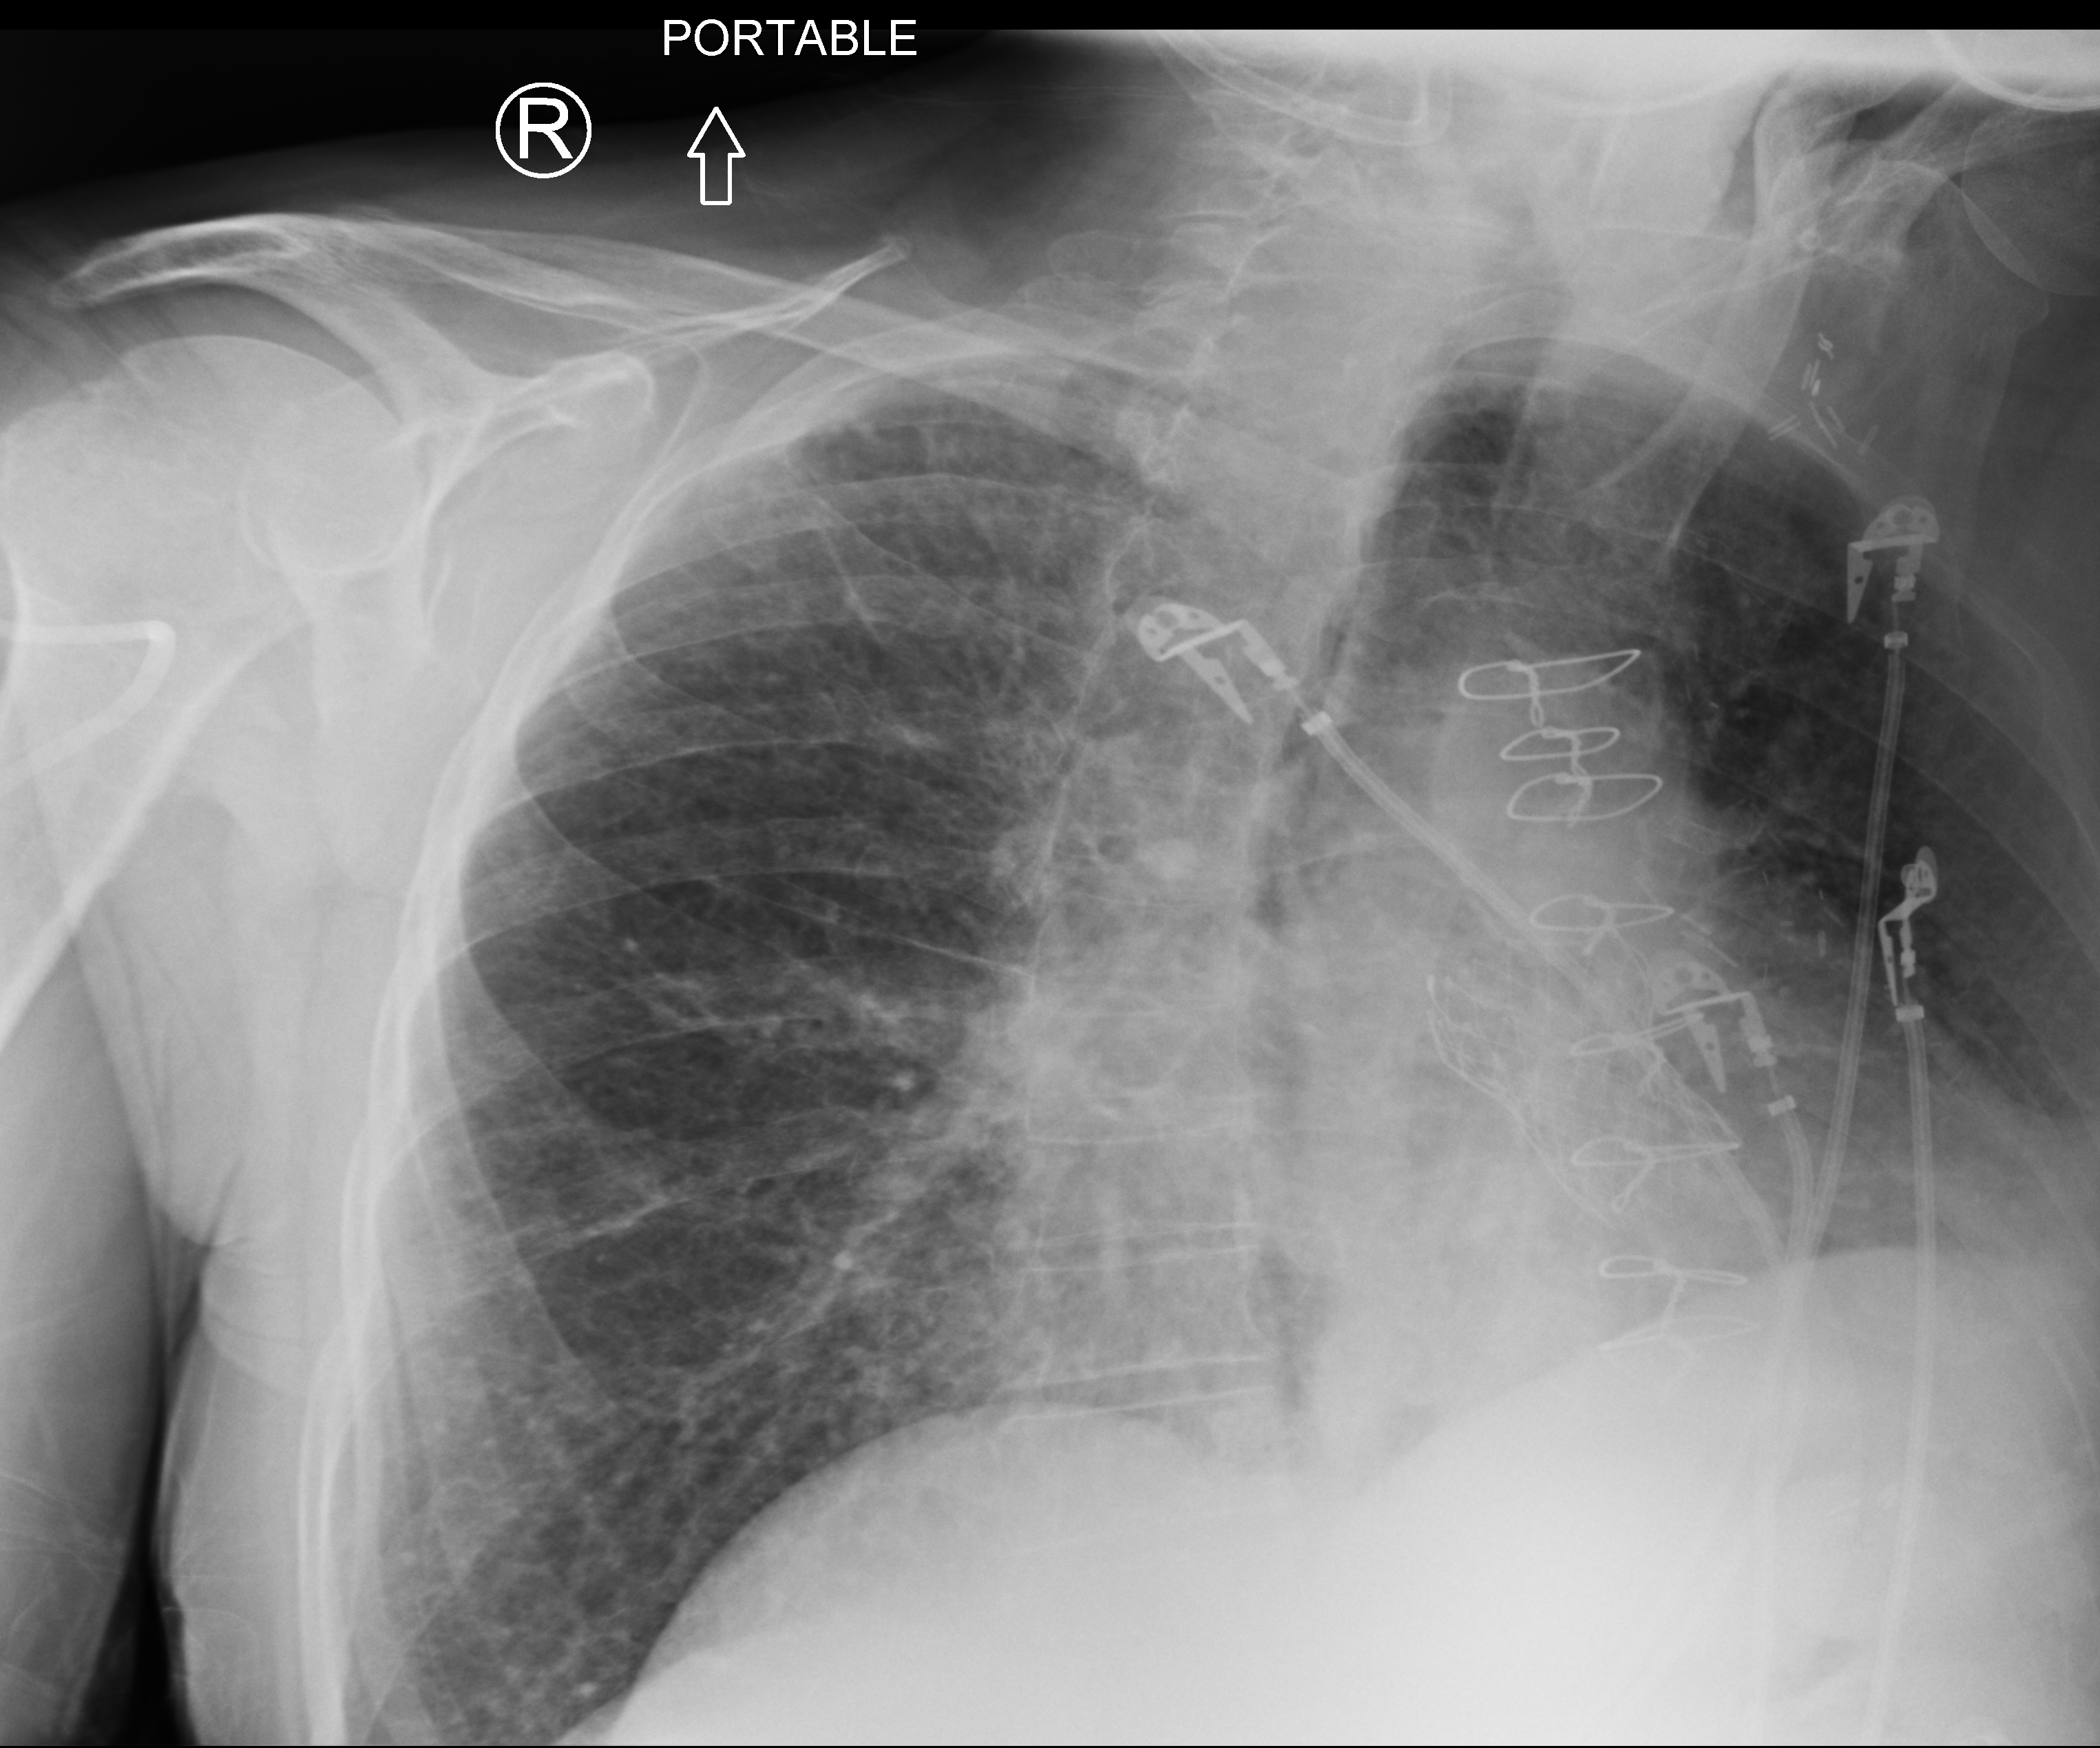
Chest X-ray (portable), anteroposterior (AP) projection. Patient hospitalised with COVID-19; female, aged 75–90 years.
Hospital-stay facts (about this admission, not read from this image; timing relative to this image not recorded): mechanically ventilated during this hospital stay: no; other chronic lung disease (admission record): no; admitted to intensive care during this hospital stay: yes.